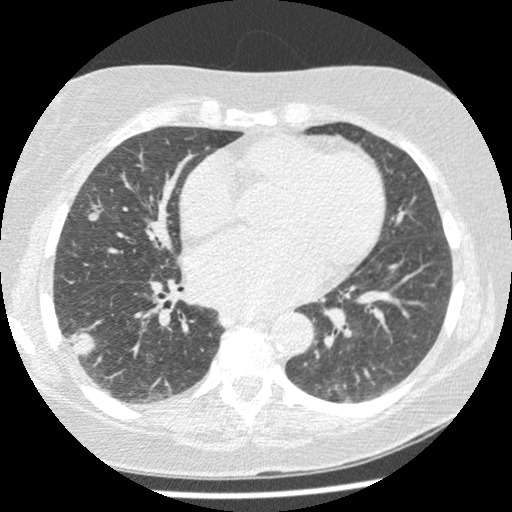
Low-dose screening chest CT, one axial slice. Position 112 of 241 along the scan axis. 120 kVp. Lung window (W 1500 / L -600 HU). 512 × 512 image matrix, field of view 305 × 305 mm.
Structures marked on this image (manually delineated by an expert):
- lesion 1 (tumor, lower lobe of right lung): box from (x=70, y=332) to (x=96, y=360) px